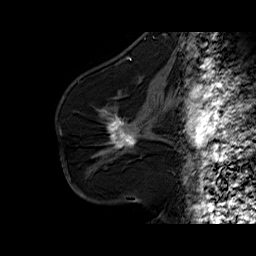
Breast MRI (dynamic contrast-enhanced), one sagittal slice; slice 35 of 60 in the series (ordered by position); dynamic contrast-enhanced series, time point 2 of 6 at this slice position (early post-contrast); 1.5 T; TE 6.3 ms, TR 32.5 ms; 256 × 256 image matrix. Female patient. From the clinical record (not read from this slice): setting: breast cancer imaged before/during neoadjuvant chemotherapy; receptor status: HR-positive, HER2-negative.
Outlined on this slice (semi-automatically segmented with operator editing):
- analysis volume of interest (the breast-tissue region the enhancement analysis was run in; not a lesion): bounding box <94,103,161,164> (left, top, right, bottom; pixels)
- tumour enhancement mask (voxels above the 100 % enhancement threshold inside the analysis volume of interest): <107,116,136,148>